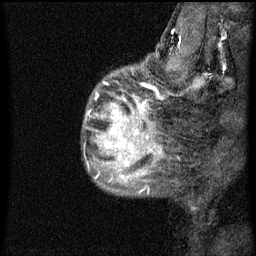
Breast MRI (dynamic contrast-enhanced), one sagittal slice. Slice 12 of 60 in the series (ordered by position). Dynamic contrast-enhanced series, image 2 of 3 at this slice position (ordered by acquisition). 1.5 T. TE 4.2 ms, TR 8 ms. 256 × 256 image matrix, field of view 180 × 180 mm. Patient: female, 50 years.
Outlined on this slice (semi-automatically segmented with operator editing):
- analysis volume of interest (the breast-tissue region the enhancement analysis was run in; not a lesion): box from (x=88, y=70) to (x=141, y=187) px
- tumour enhancement mask (voxels above the 70 % enhancement threshold inside the analysis volume of interest): (x=107, y=106)–(x=141, y=159)